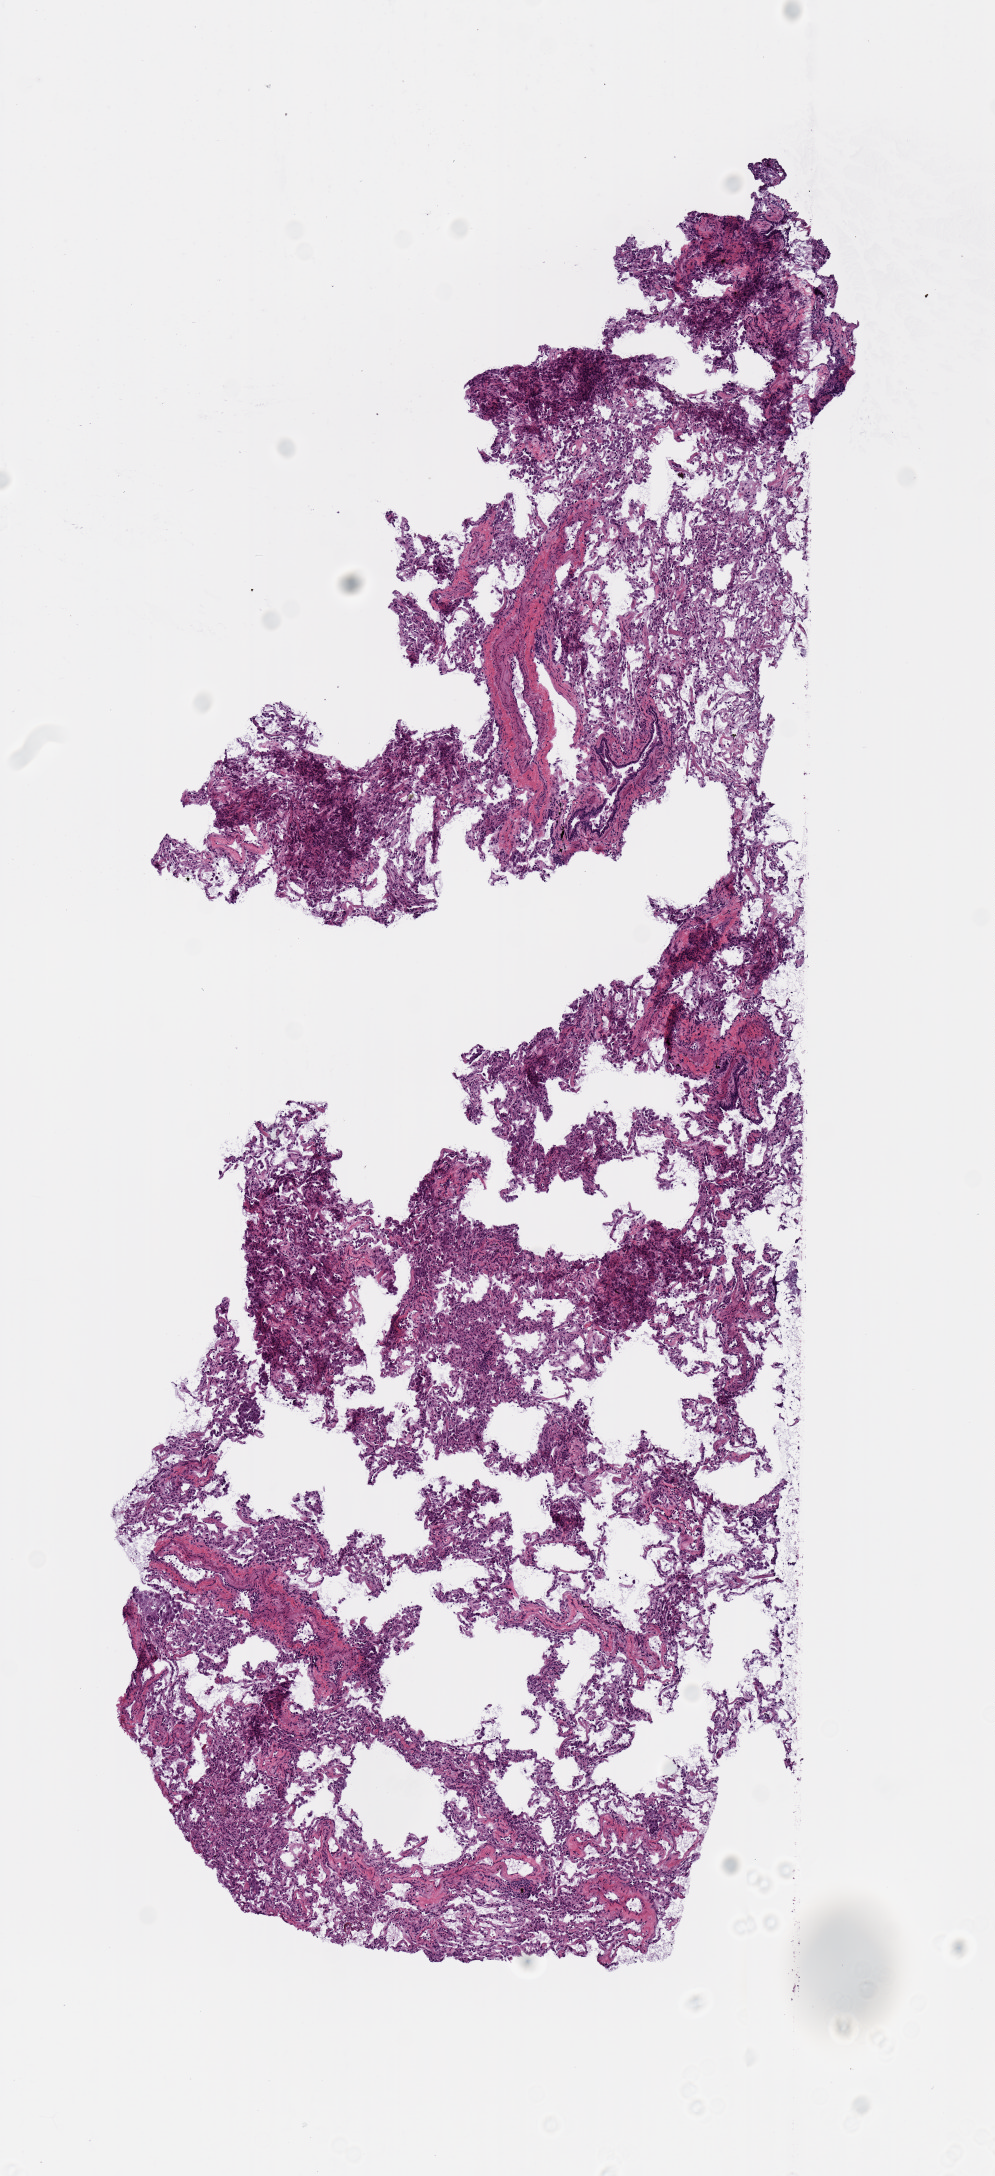
Whole-slide histology image, Hematoxylin and eosin (H&E) stained — a low-resolution overview of the entire scanned area, about 3.9 x 8.6 mm, frozen section from the top of the tissue portion, solid tissue normal (non-tumour tissue) sample from the lung. Female patient; age at initial diagnosis 53 years.
This section: solid tissue normal (non-tumour) sample from the same patient. Patient diagnosis: Adenocarcinoma, NOS.